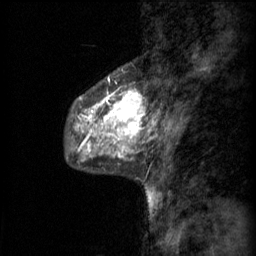
Breast MRI (dynamic contrast-enhanced), one sagittal slice. Slice 21 of 60 in the series (ordered by position). 3 images stored at this slice position (order not interpretable as contrast timing). 1.5 T. TE 4.2 ms, TR 11 ms. 2 mm slice thickness. 256 × 256 image matrix, field of view 200 × 200 mm. Female patient, age 48 years.
Outlined on this slice (semi-automatic segmentation, software-assisted and operator-edited):
- analysis volume of interest (the breast-tissue region the enhancement analysis was run in; not a lesion): bounding box <72,76,144,147> (left, top, right, bottom; pixels)
- tumour enhancement mask (voxels above the 70 % enhancement threshold inside the analysis volume of interest): <77,78,144,147>